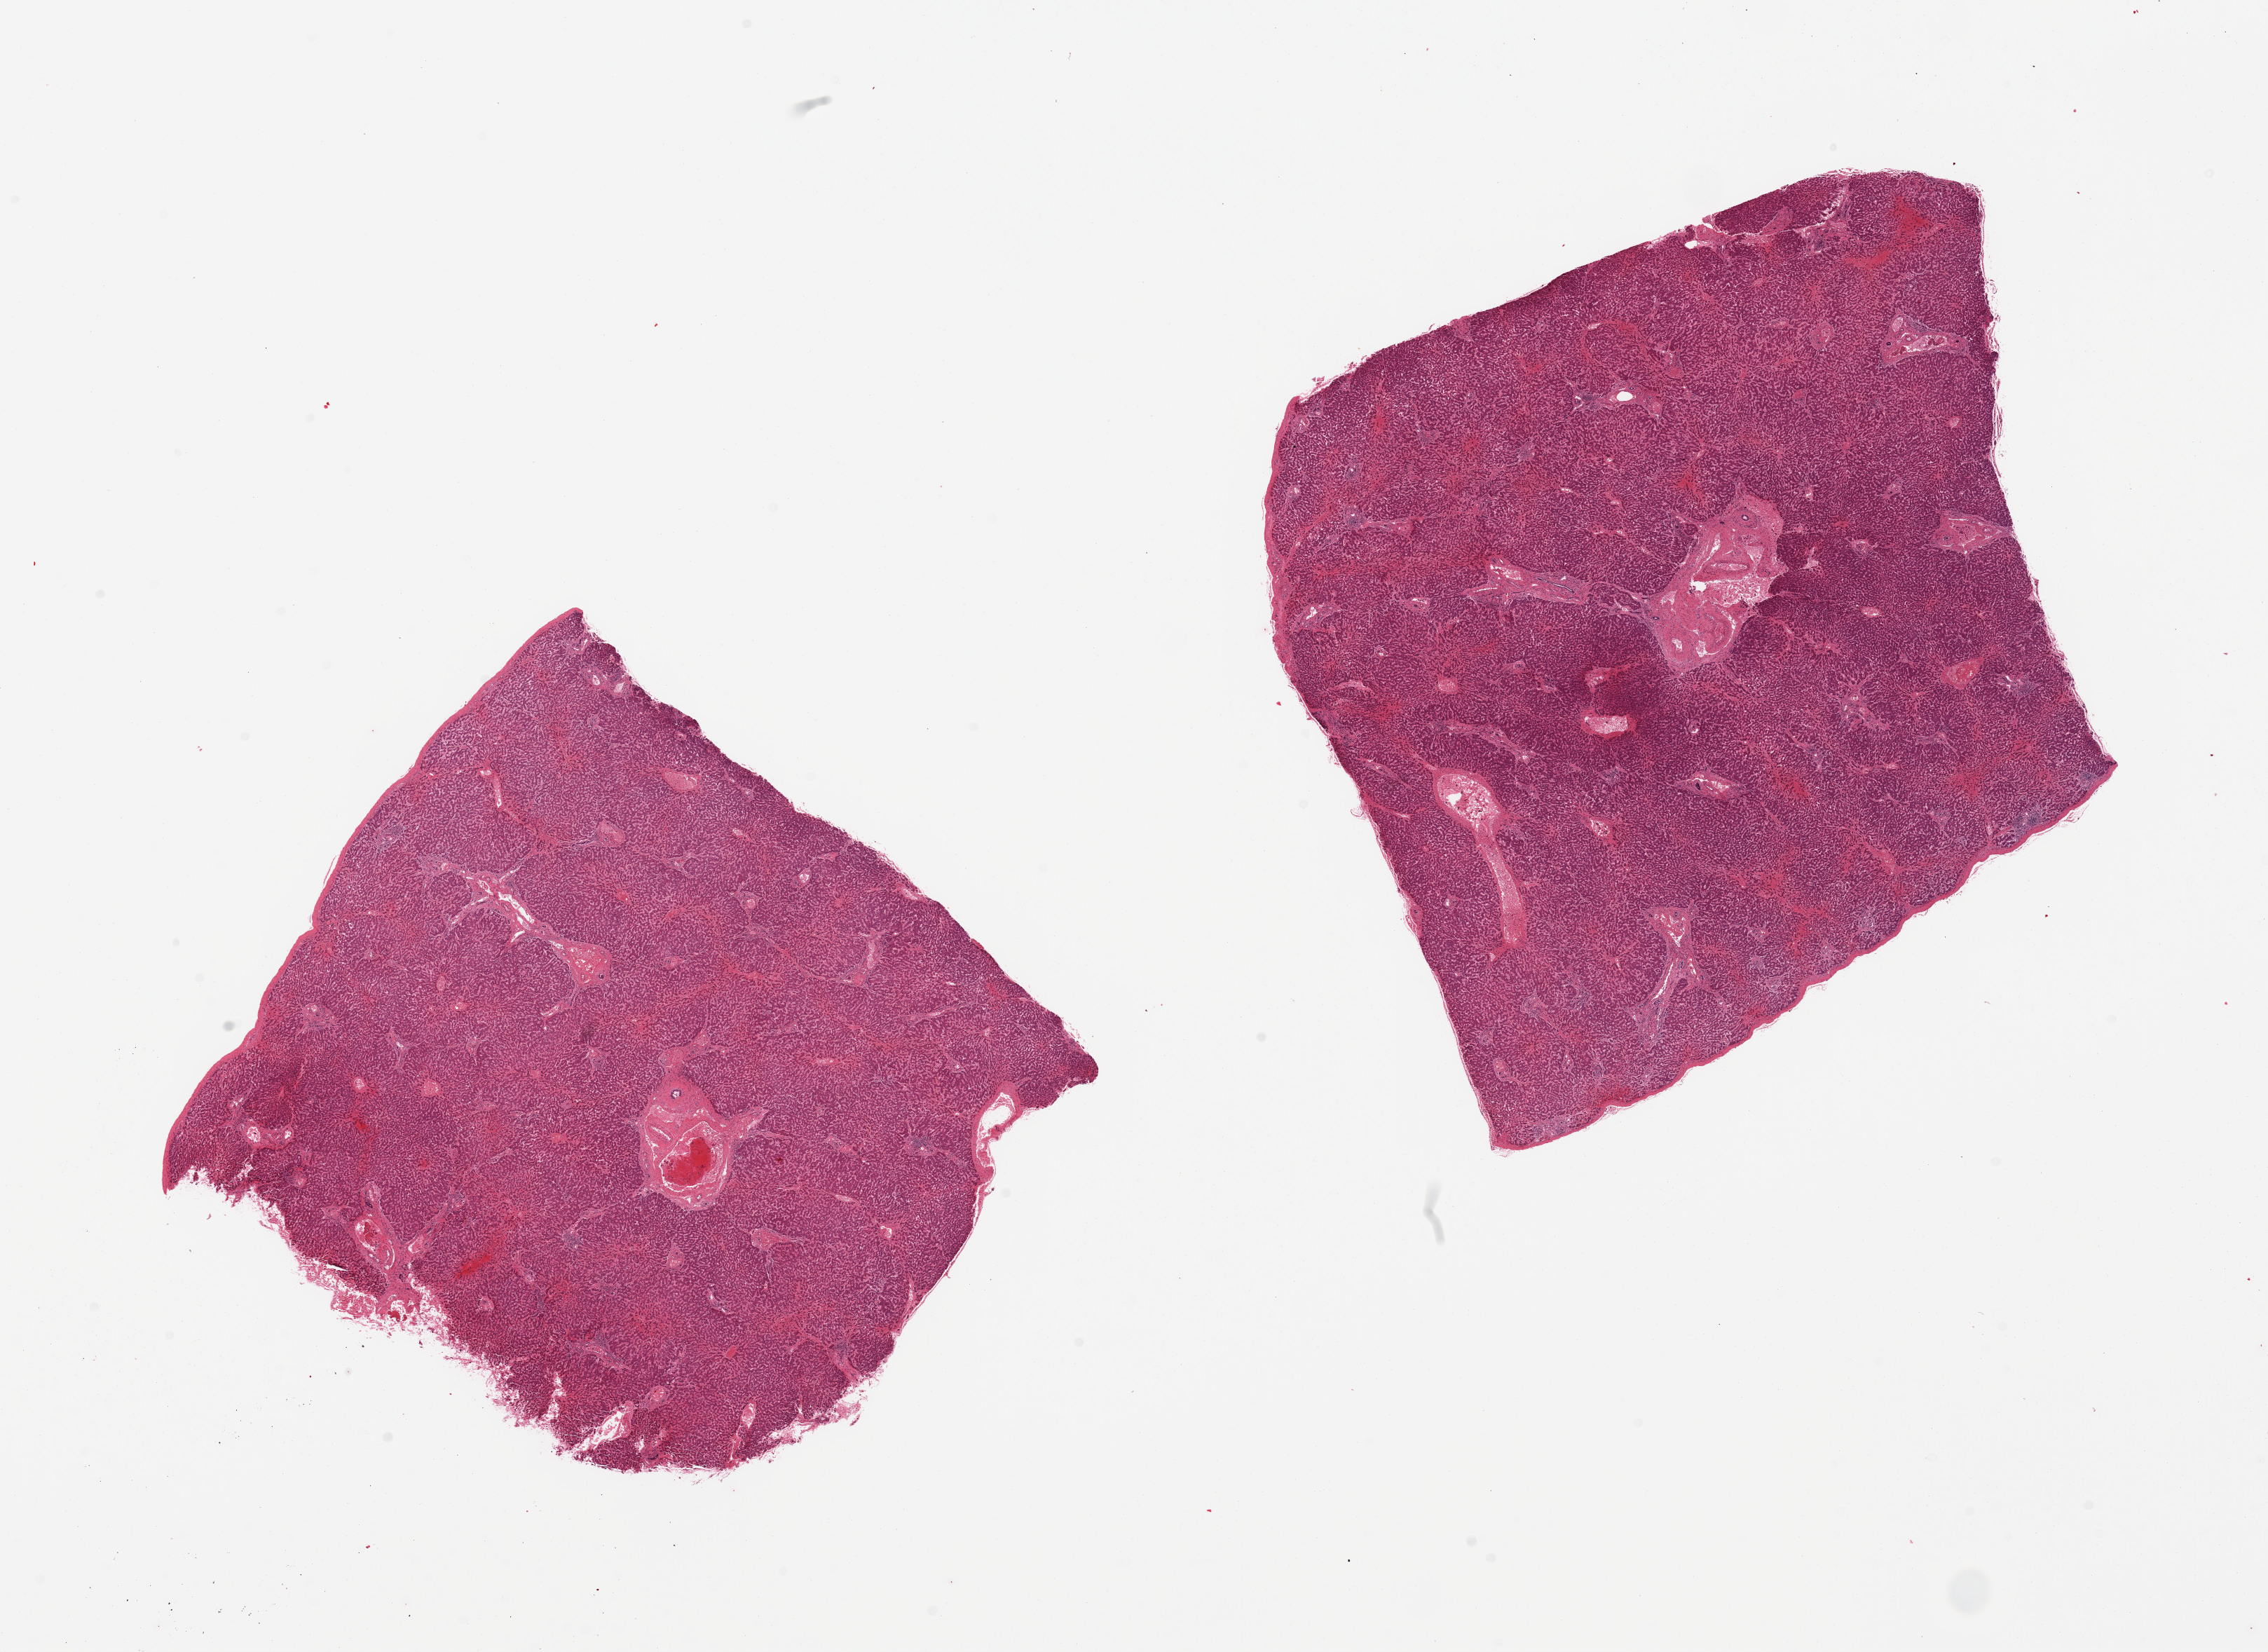
Haematoxylin and eosin whole-slide image, a low-resolution overview of the entire scanned area, about 25.6 x 18.6 mm; PAXgene-fixed paraffin-embedded (PFPE) section; target tissue: liver; tissue donor sample. Donor sex: female.
Review note (as recorded): 2 pieces; capsule [not target] on both pieces.